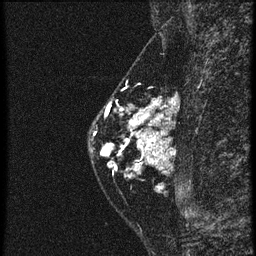
Breast MRI (dynamic contrast-enhanced), one sagittal slice. Slice 21 of 60 in the series (ordered by position). 4 images stored at this slice position (order not interpretable as contrast timing). 1.5 T. TE 4.2 ms, TR 20.4 ms. 1.5 mm slice thickness. 256 × 256 image matrix. Female patient, age 46 years. From the clinical record (not read from this slice): setting: breast cancer imaged before/during neoadjuvant chemotherapy; receptor status: triple-negative.
Annotated regions visible in this slice (semi-automatic segmentation, software-assisted and operator-edited):
- analysis volume of interest (the breast-tissue region the enhancement analysis was run in; not a lesion): bounding box [x1, y1, x2, y2] px = [88, 82, 167, 185]
- tumour enhancement mask (voxels above the 90 % enhancement threshold inside the analysis volume of interest): [102, 104, 161, 177]